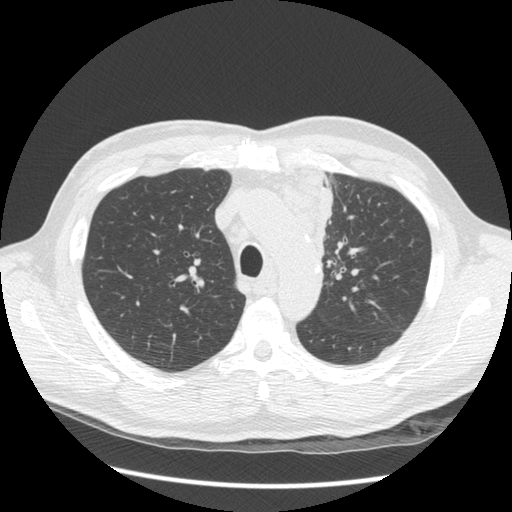
Low-dose screening chest CT, one axial slice. Slice 103 of 136 in the series (ordered by position). Reconstruction kernel STANDARD. 120 kVp. Lung window (W 1500 / L -600 HU). 2.5 mm slice thickness. 512 × 512 image matrix, field of view 360 × 360 mm.
Structures marked on this image (manually delineated by an expert):
- lesion 1 (tumor, upper lobe of left lung): bounding box (x1, y1, x2, y2) in pixels: (290, 172, 333, 263)